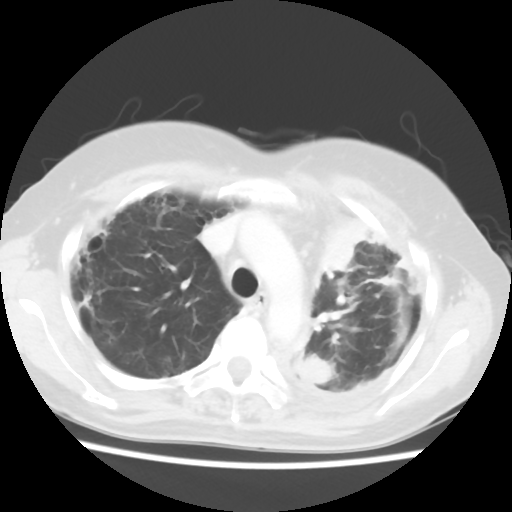
Chest CT, one axial slice. Position 41 of 56 along the scan axis. Reconstruction kernel STANDARD. Lung window (W 1500 / L -600 HU). 5 mm slice thickness. 512 × 512 image matrix. Patient: female, 56 years. From the clinical record (not read from this slice): clinical TNM (as recorded): T1c N0 M1.
Annotated regions visible in this slice (rectangle marked by the reading radiologist):
- lung tumour (recorded histology: adenocarcinoma): bounding box (x1, y1, x2, y2) in pixels: (316, 210, 363, 277)